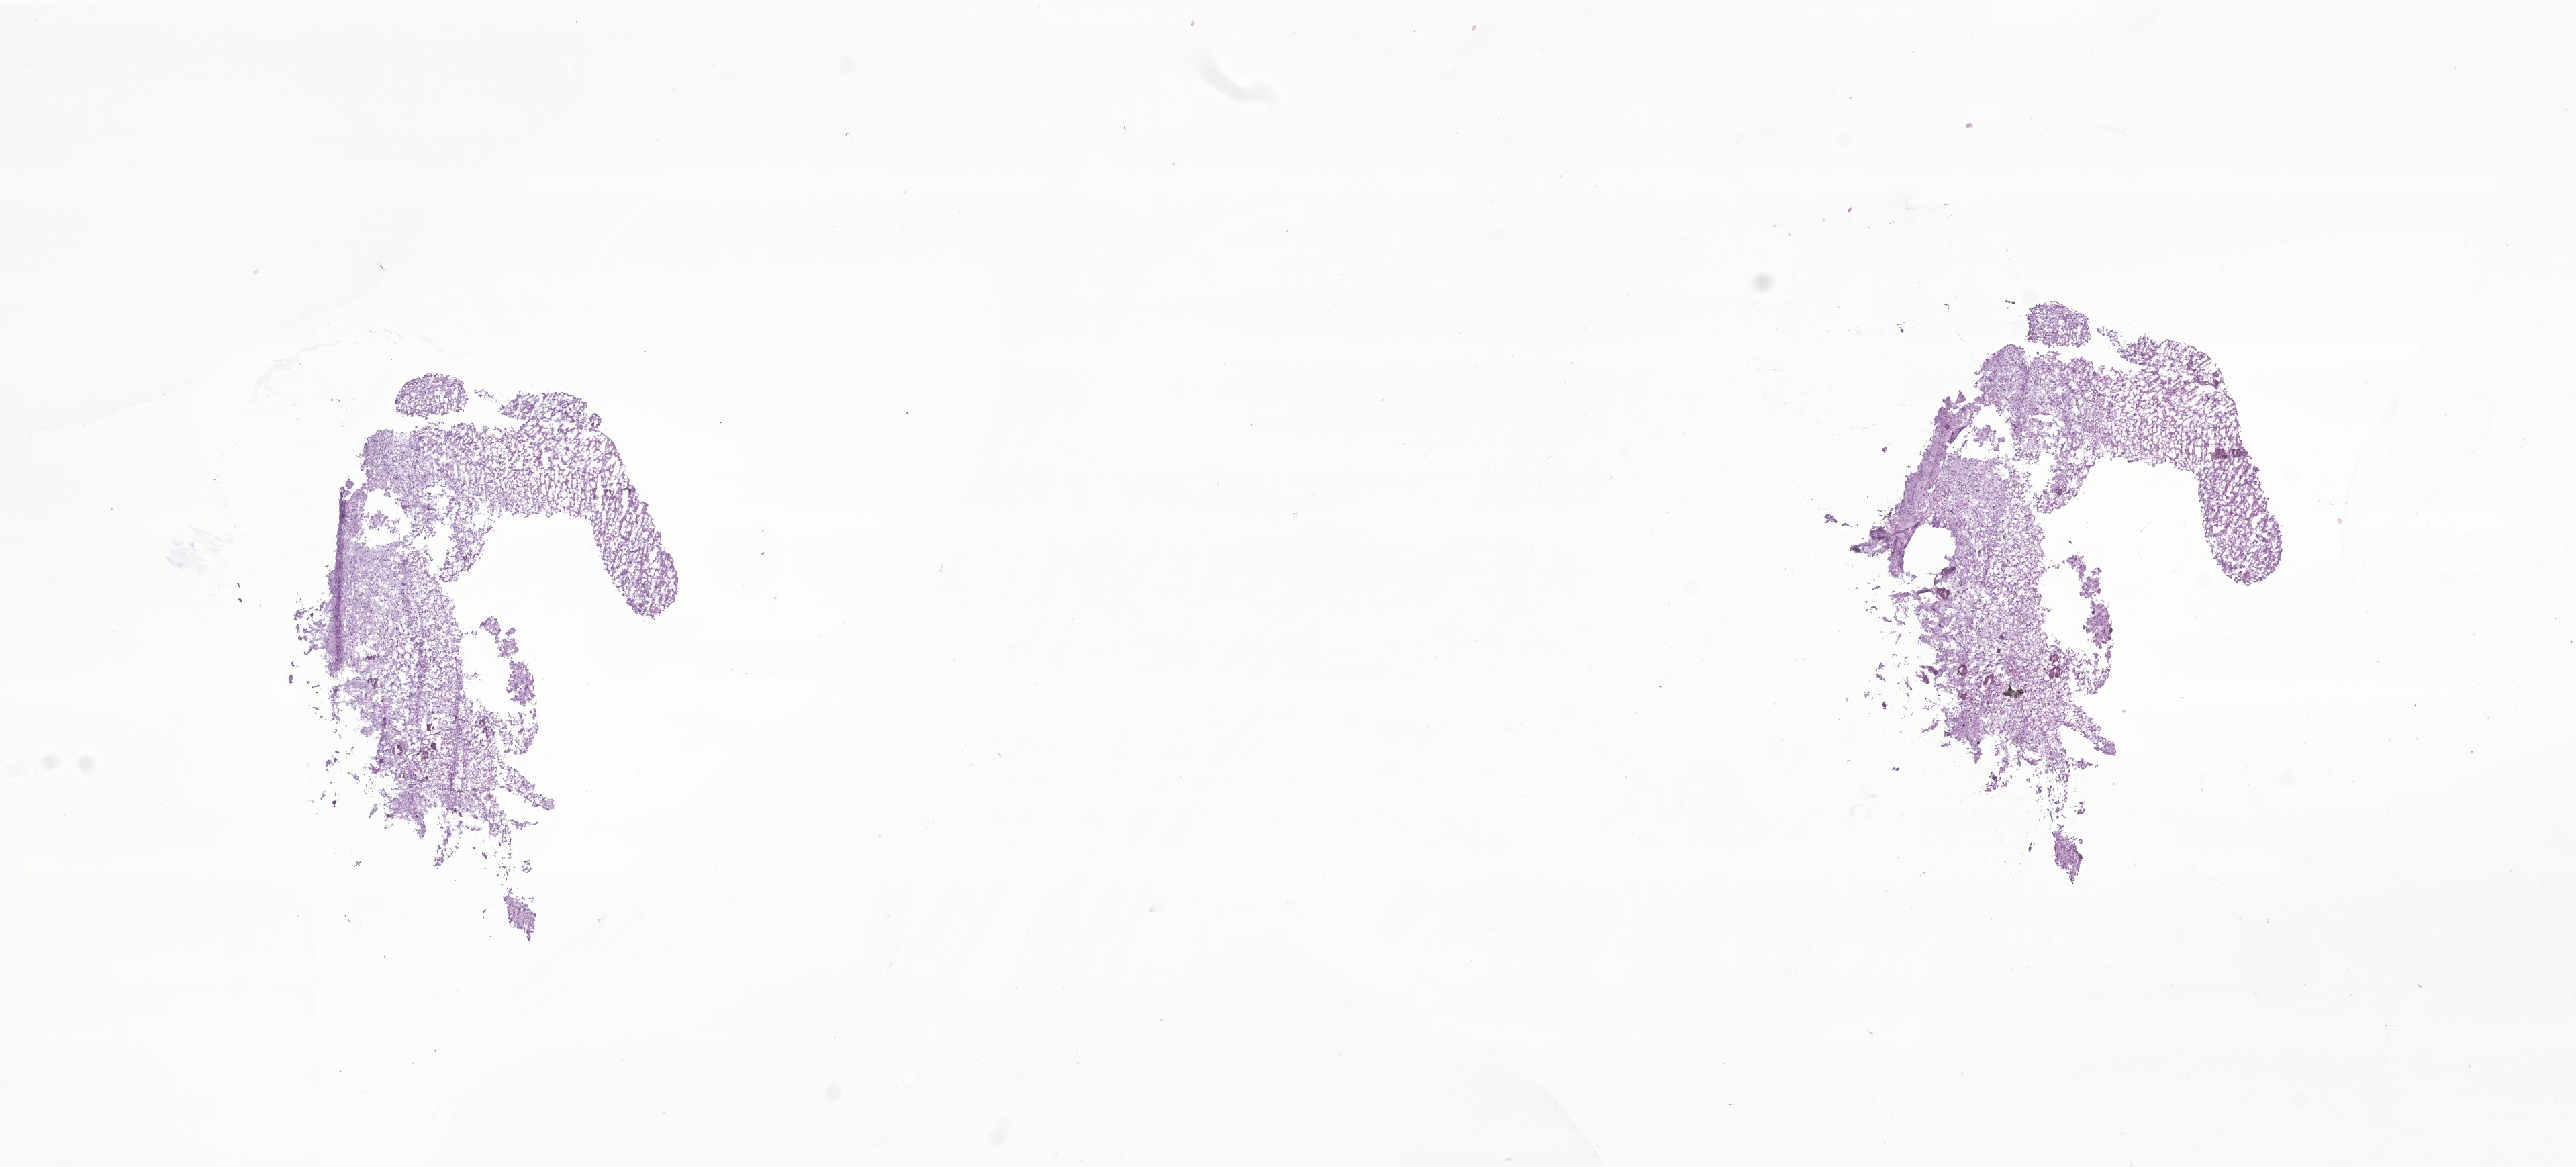
Whole-slide image, haematoxylin and eosin stain of tumor tissue from the brain — whole scanned area (about 16.2 x 7.3 mm) shown as a low-resolution overview; frozen section. Female patient, age 204 months (17 years).
- recorded diagnosis: Pilocytic astrocytoma